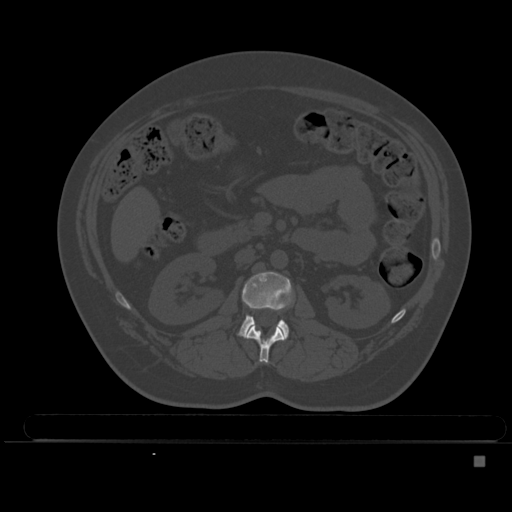
CT including the spine, one axial slice. Position 183 of 495 along the scan axis. Bone window (W 1800 / L 400 HU). 1.5 mm slice thickness. 512 × 512 image matrix. Female patient, age 33 years. Case-level facts recorded for this patient, not image findings: primary cancer: breast.
Annotated regions visible in this slice (semi-automatic segmentation, software-assisted and operator-edited):
- L1 vertebra: bounding box <244,324,285,363> (left, top, right, bottom; pixels)
- L2 vertebra: <239,271,292,339>